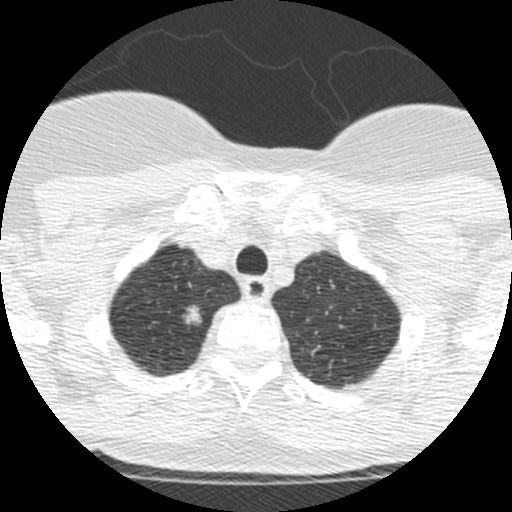
Low-dose screening chest CT, one axial slice. Position 215 of 250 along the scan axis. Lung window (W 1500 / L -600 HU). 1.25 mm slice thickness. 512 × 512 image matrix, field of view 257 × 257 mm.
Structures marked on this image (manually delineated by an expert):
- lesion 1 (tumor, upper lobe of right lung): bounding box (x1, y1, x2, y2) in pixels: (183, 305, 201, 324)